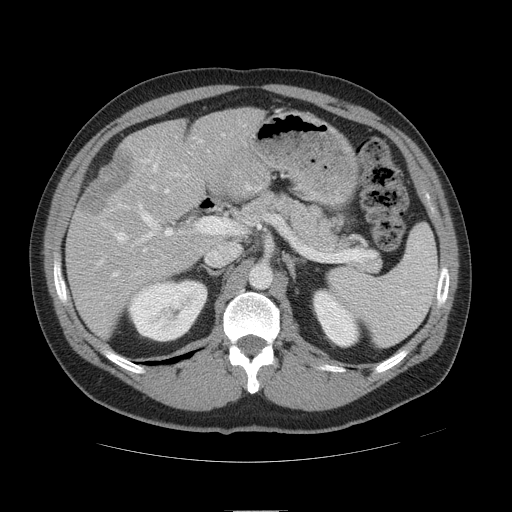
Contrast-enhanced abdominal CT, one axial slice. Slice 28 of 49 in the series (ordered by position). Soft-tissue window (W 400 / L 40 HU). 5 mm slice thickness. 512 × 512 image matrix, field of view 425 × 425 mm. Male patient, age 52 years. From the clinical record (not read from this slice): diagnosis: colorectal cancer liver metastases, imaged before liver resection; multiple liver metastases: yes; largest metastasis: 5.1 cm; chemotherapy before resection: yes.
Structures marked on this image (manually delineated by an expert):
- hepatic veins: bounding box (x1, y1, x2, y2) in pixels: (113, 136, 203, 277)
- liver: (68, 109, 259, 332)
- planned liver remnant (the part of the liver to remain after resection): (132, 109, 259, 201)
- portal vein (with intrahepatic branches): (106, 159, 212, 298)
- liver metastasis: (81, 148, 135, 218)